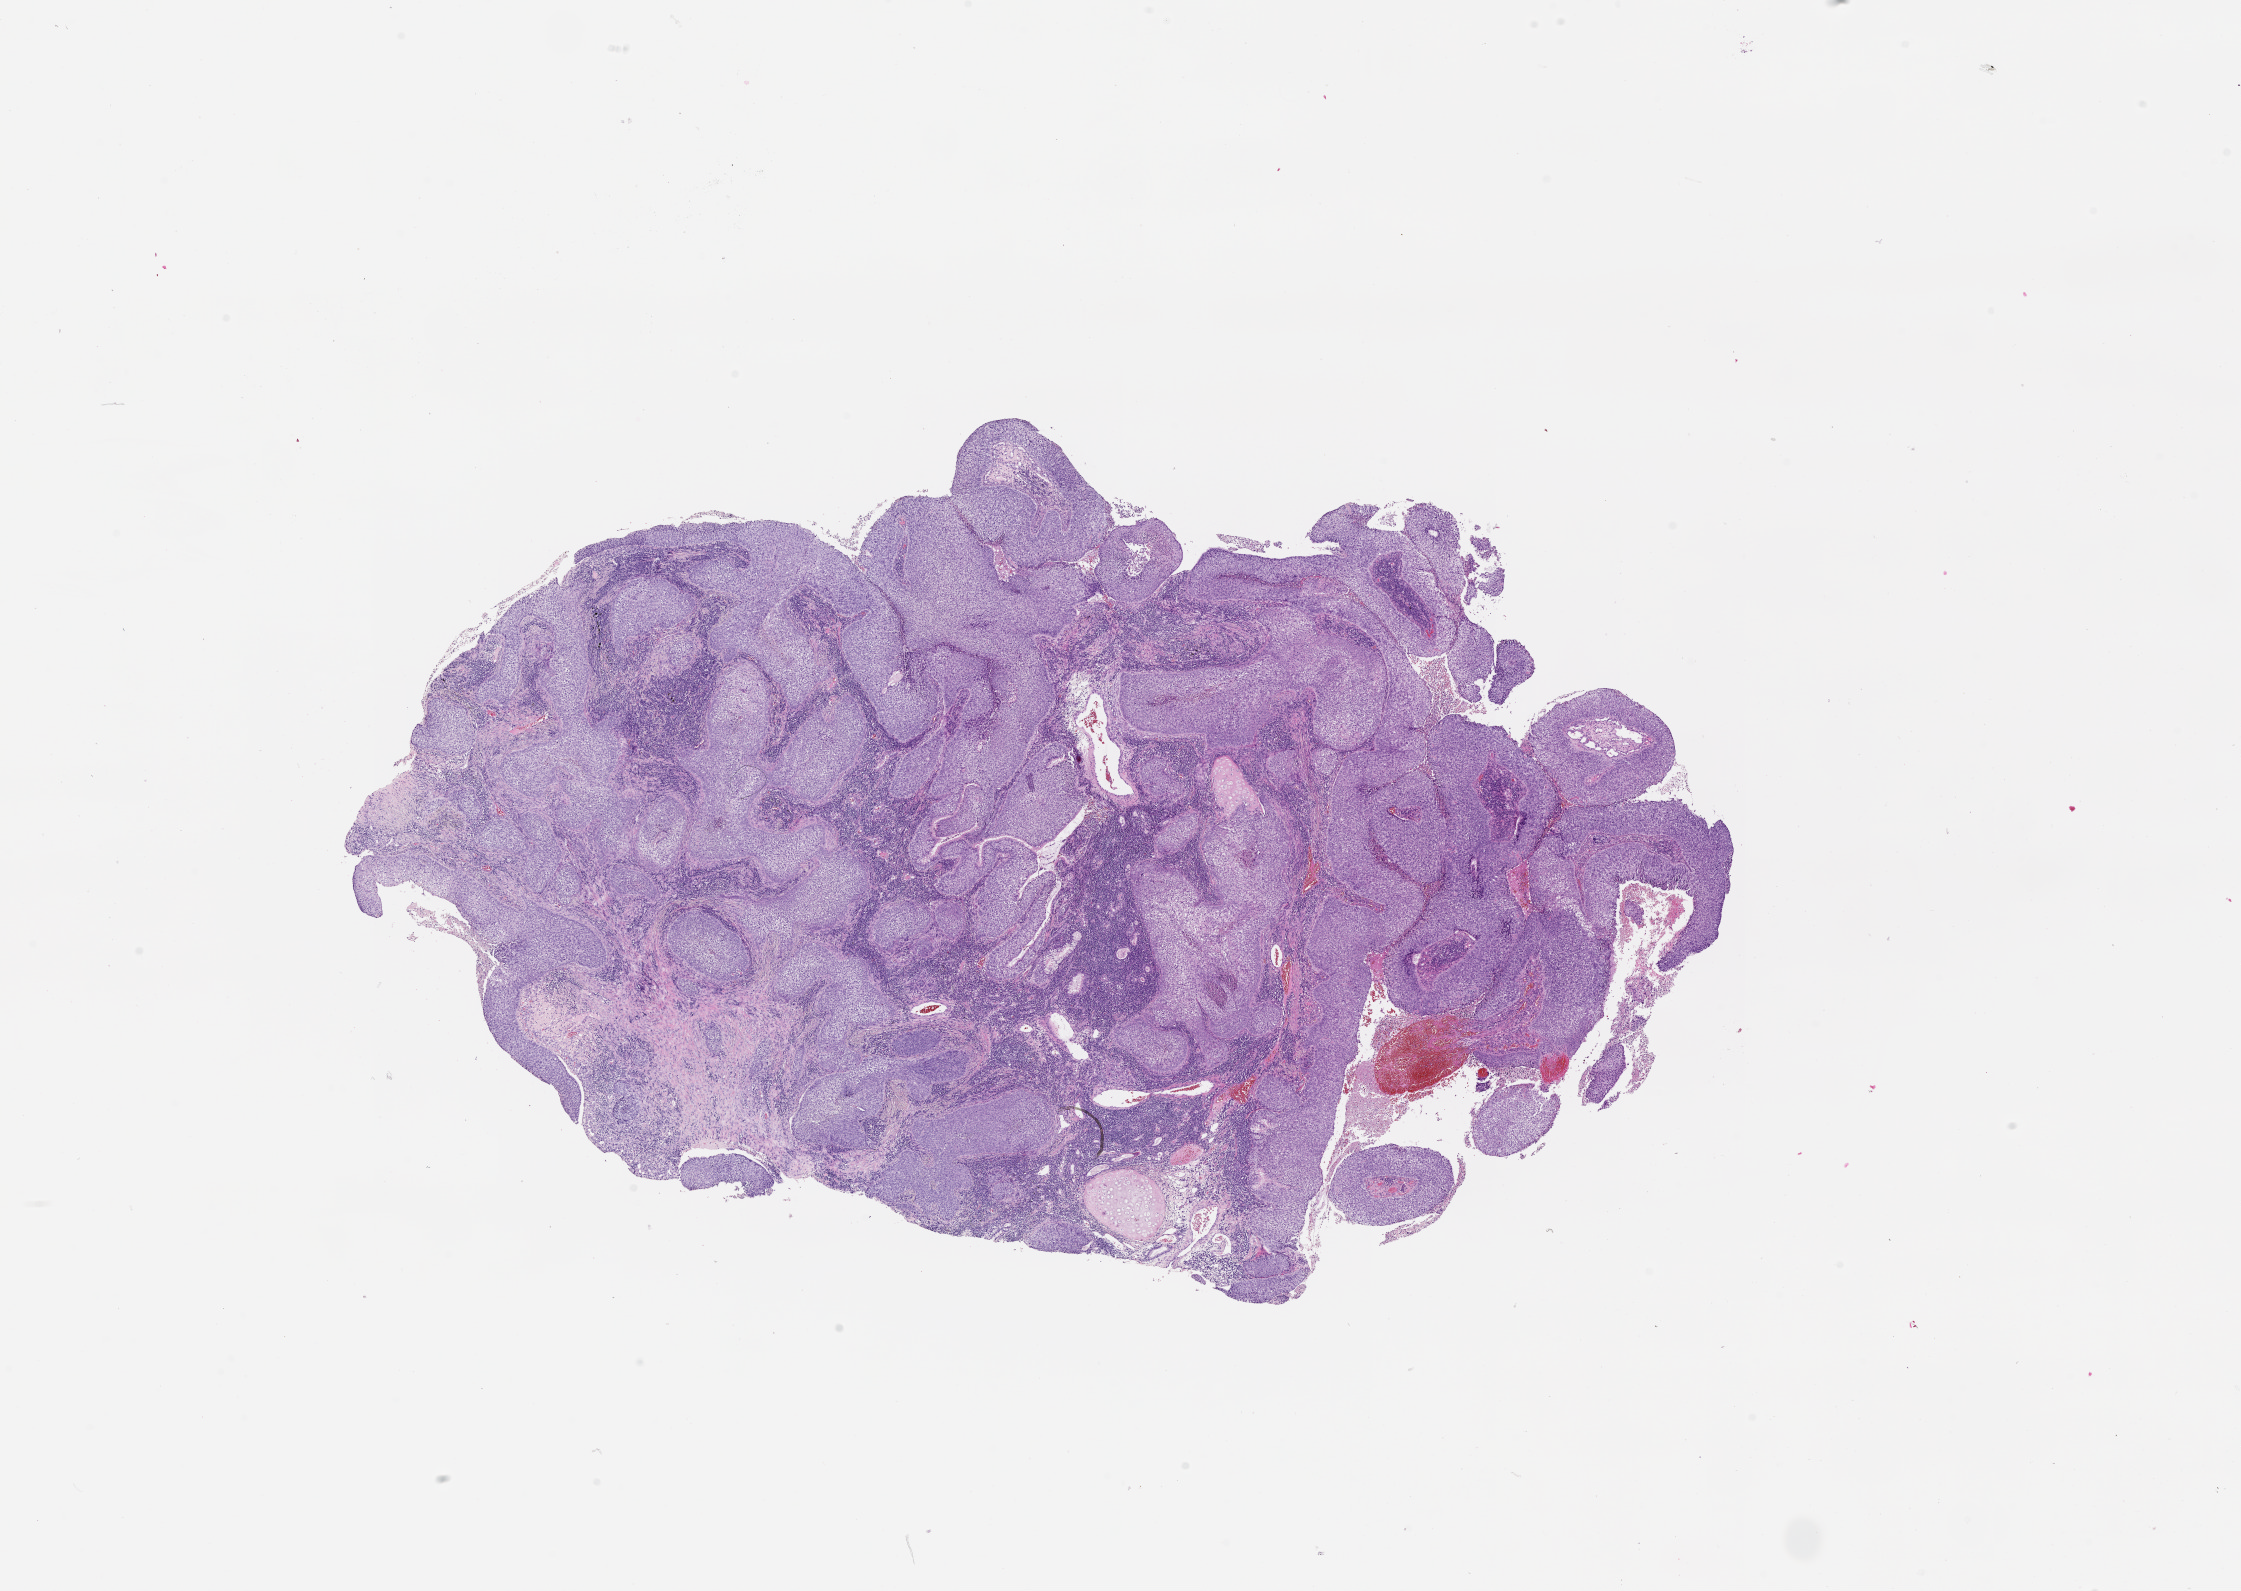
Digitized H&E tissue section (whole slide) — shown as a low-resolution overview of the whole scanned area (about 18.0 x 12.8 mm, acquisition: 20x scan), lung, tumour tissue. 60-year-old male patient.
Patient diagnosis (cohort enrolment): squamous cell carcinoma (lung).